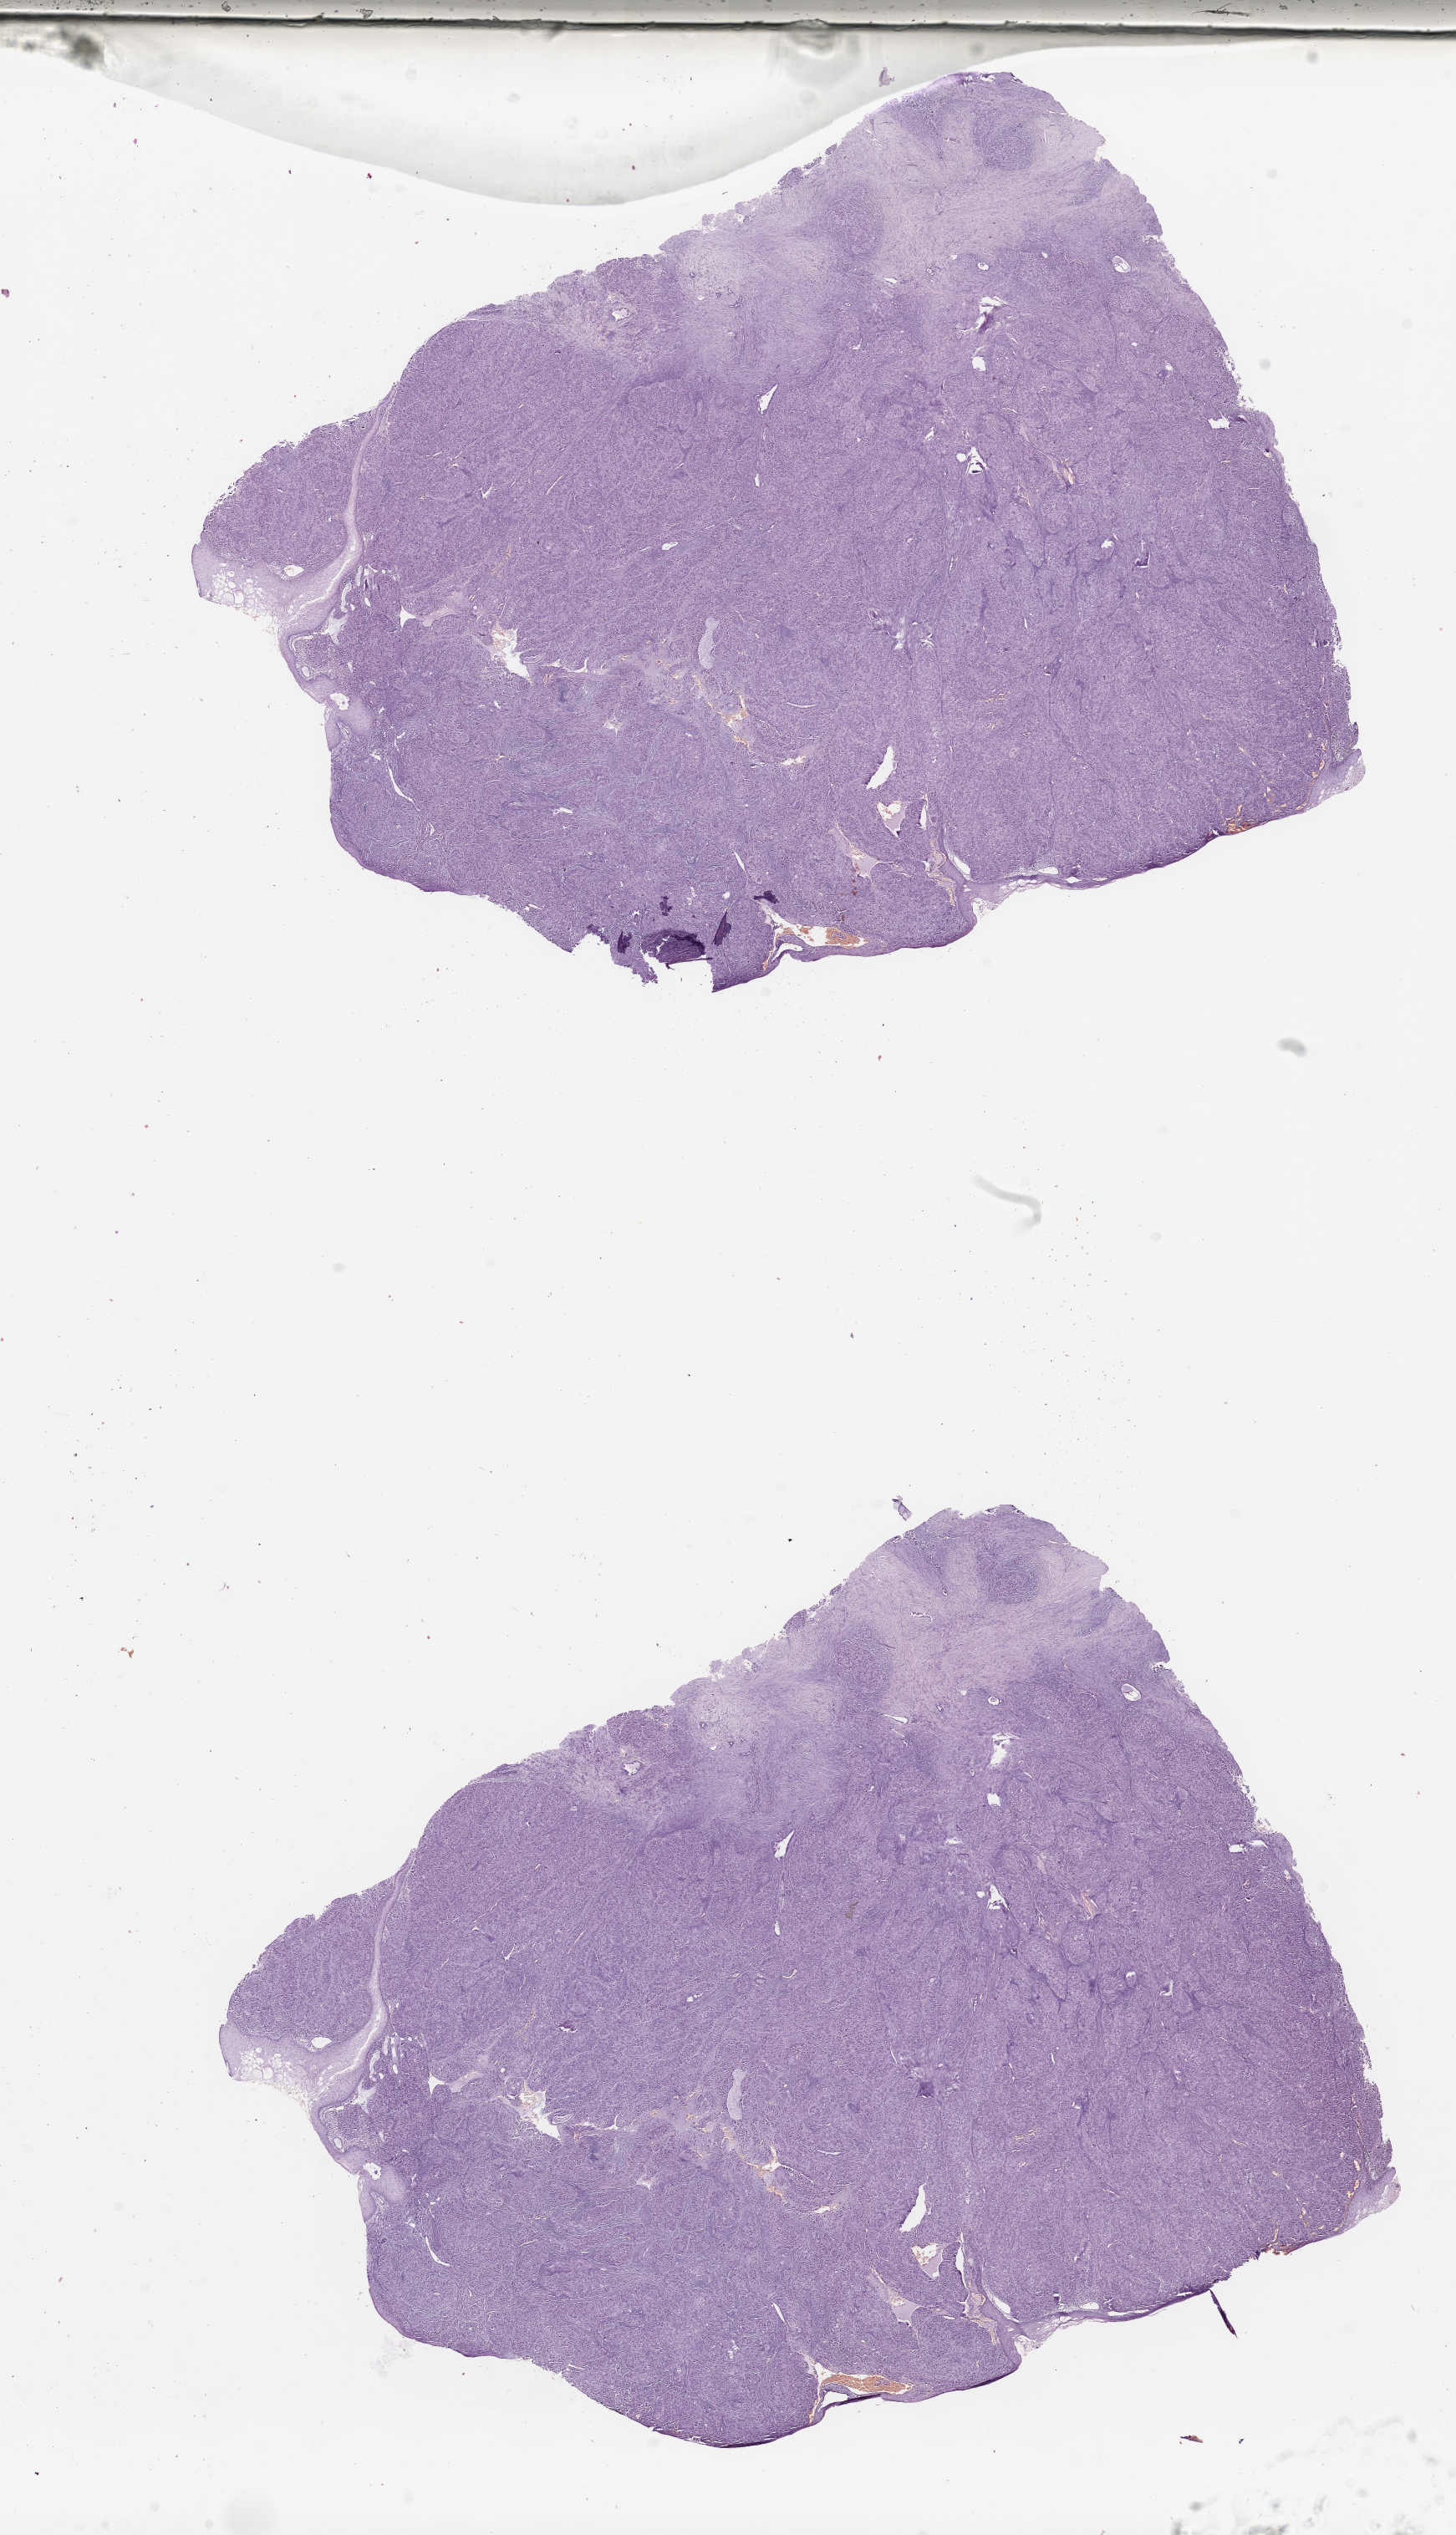
Whole-slide histology image, H&E, low-resolution overview of the scanned area, about 13.8 x 24.0 mm (slide scanned at 20x), head and neck, tissue type not recorded. Male, 64 y/o.
- patient diagnosis: Squamous cell carcinoma, NOS (base of tongue, NOS)